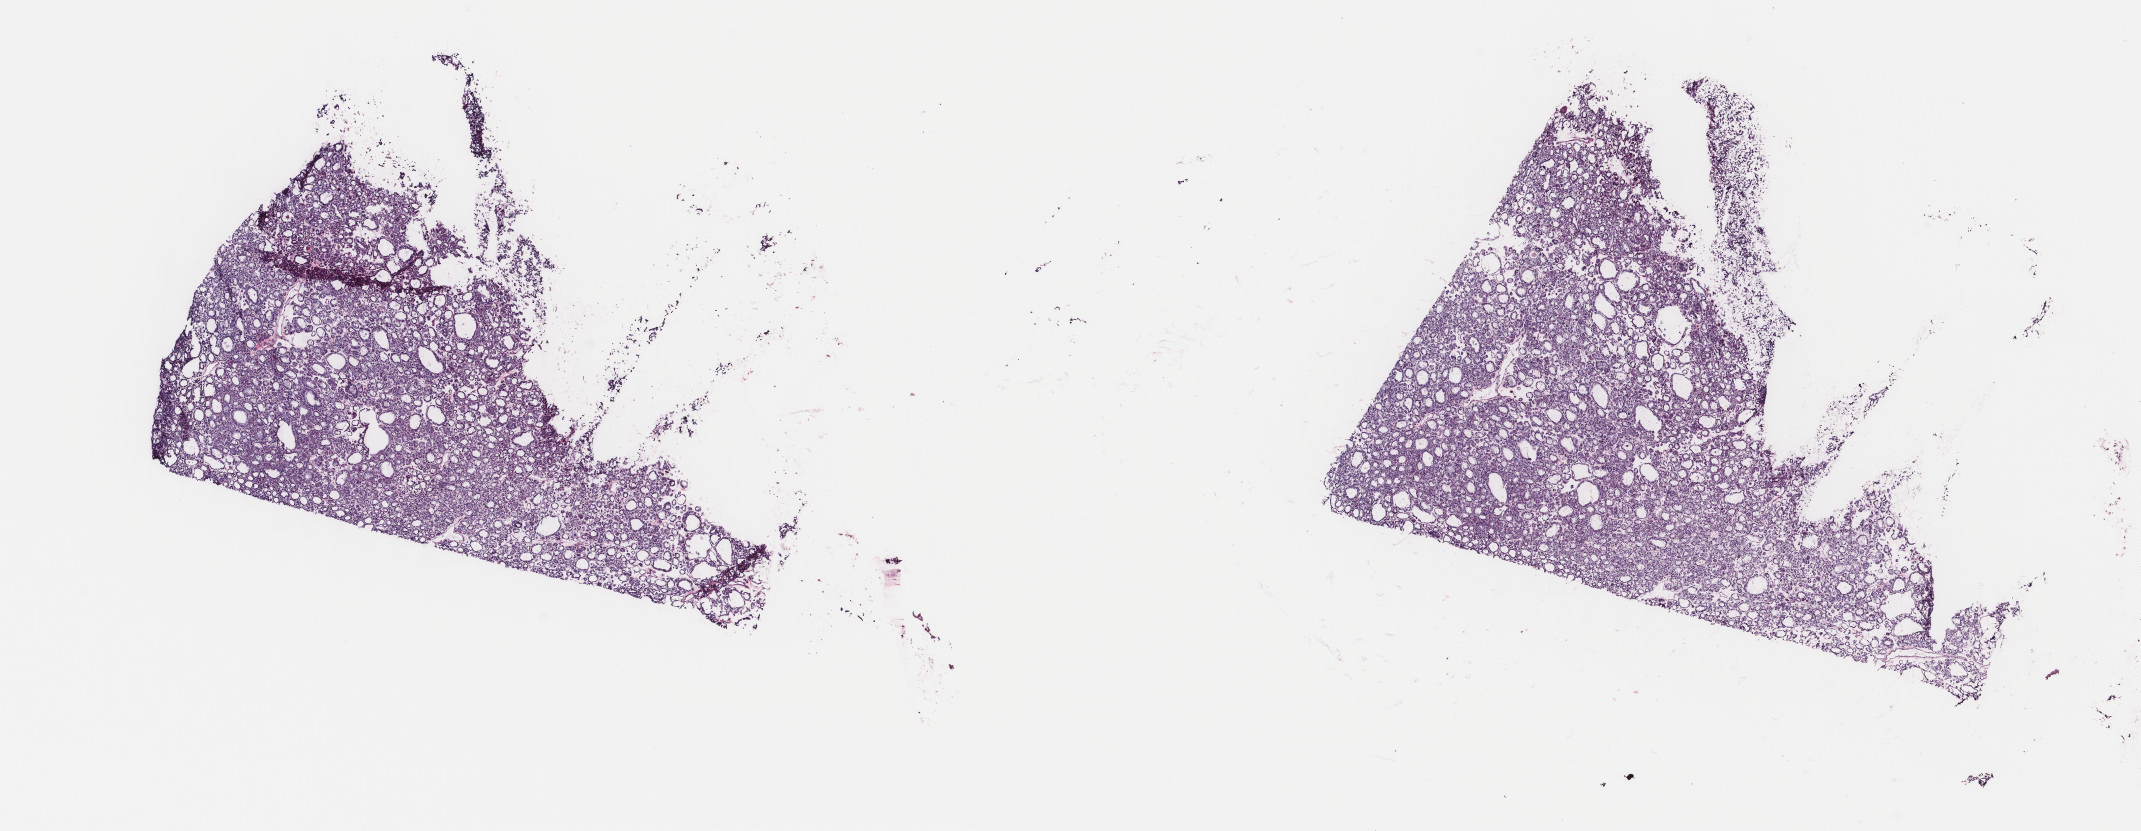
Whole-slide histology image, H&E-stained — shown as a low-resolution overview of the whole scanned area (about 17.0 x 6.6 mm). Frozen section from the top of the tissue portion. Primary tumour sample from the thyroid. Female, age 46 years at initial diagnosis. Composition of this section per pathologist review: tumour cells 100%, tumour nuclei 95%, normal cells 0%, stromal cells 0%, necrosis 0%. Inflammatory infiltration, as recorded: lymphocyte infiltration 1%, monocyte infiltration 3%, neutrophil infiltration 0%.
Laterality: right. AJCC pathologic stage: III. Histologic diagnosis: Papillary carcinoma, follicular variant (thyroid gland). TNM: T3 NX MX.